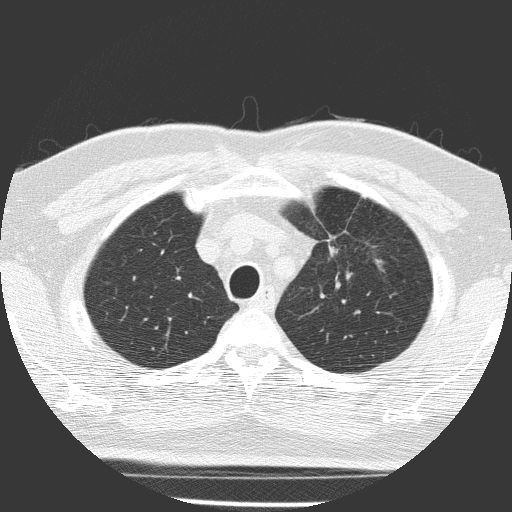
Low-dose screening chest CT, one axial slice. Position 123 of 156 along the scan axis. Lung window (W 1500 / L -600 HU). 2 mm slice thickness. 512 × 512 image matrix, field of view 309 × 309 mm.
Outlined on this slice (manually delineated by an expert):
- lesion 1 (tumor, upper lobe of left lung): bounding box (x1, y1, x2, y2) in pixels: (329, 246, 337, 255)